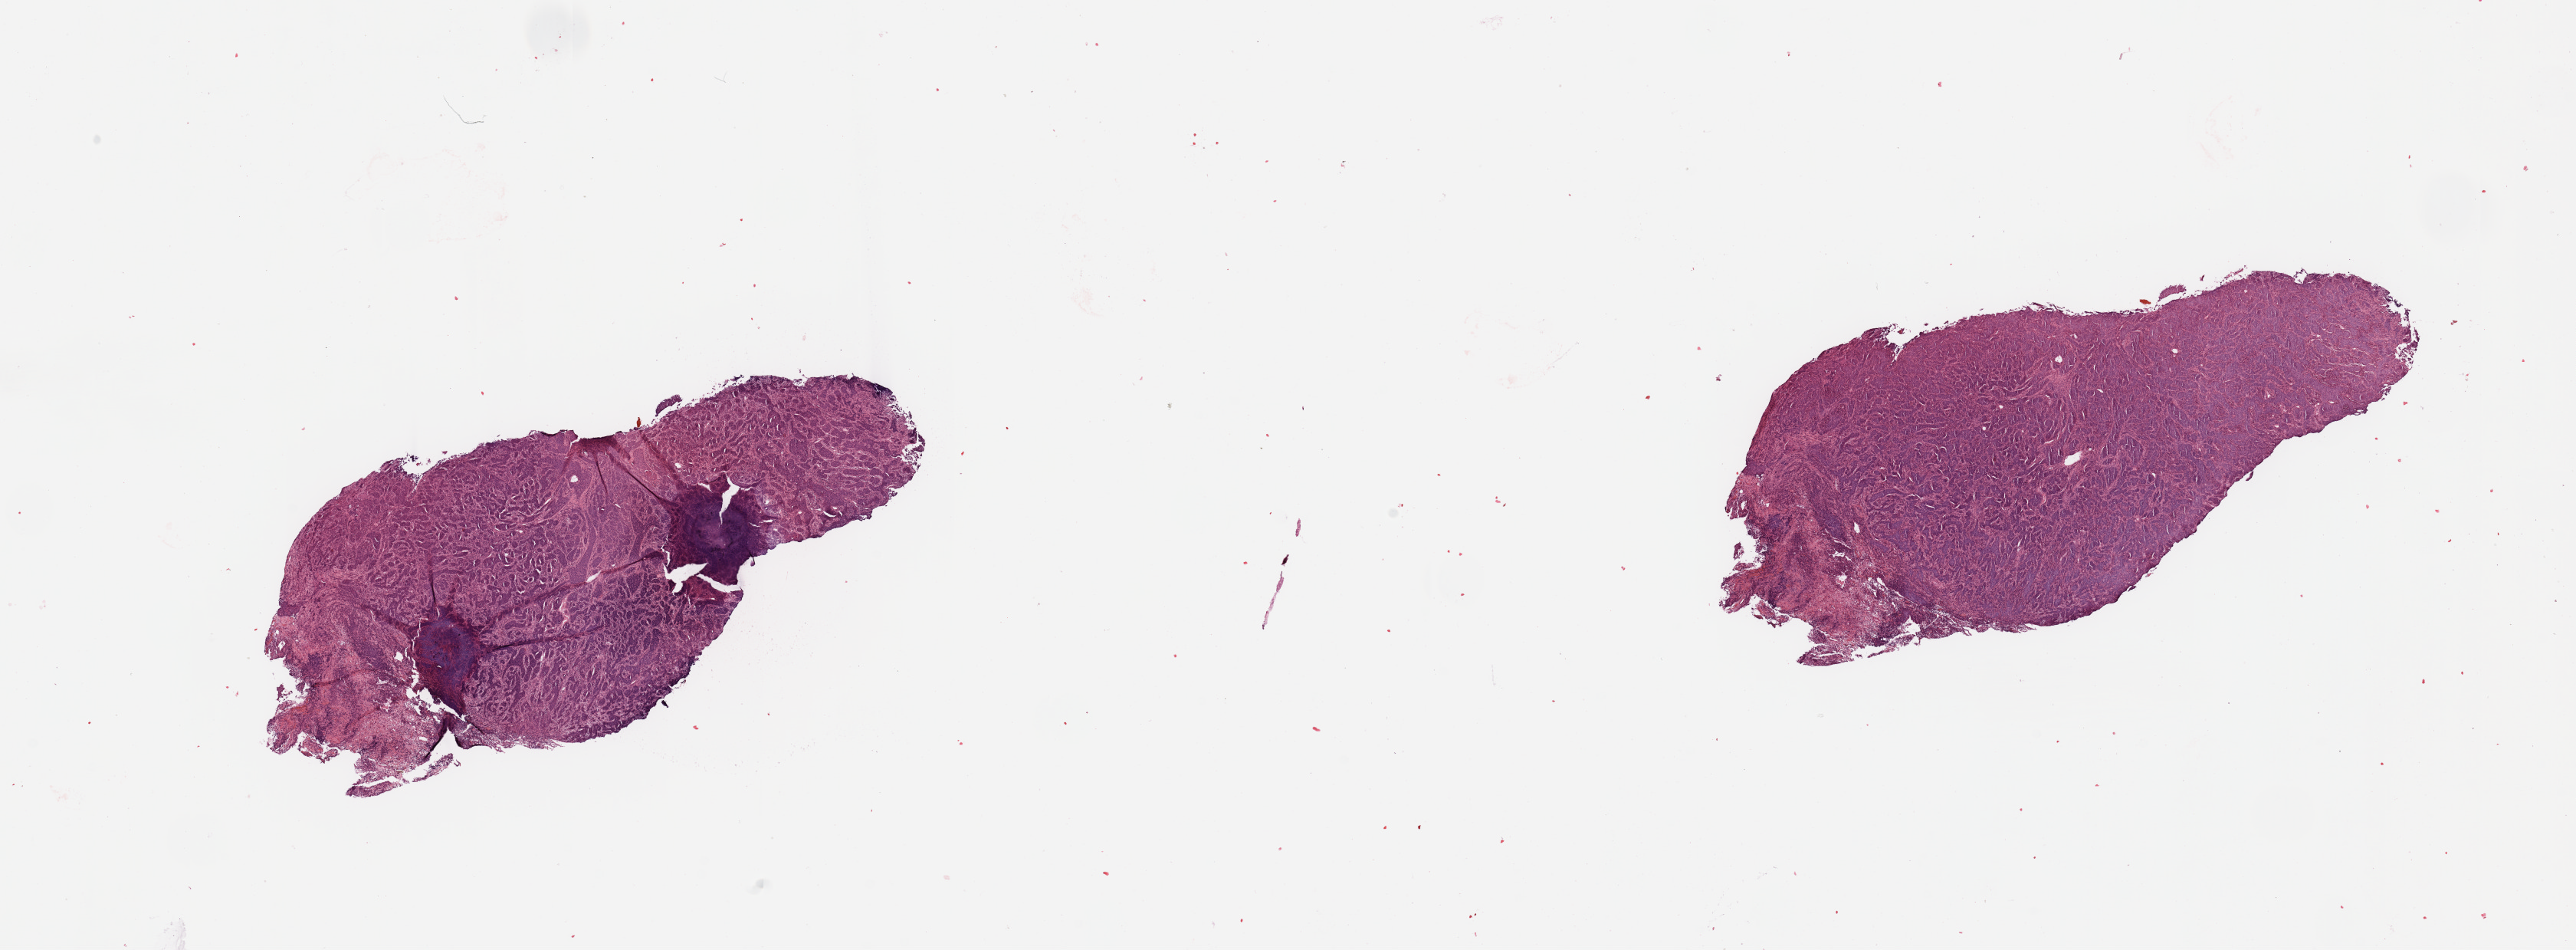
Whole-slide histology image, H&E, shown as a low-resolution overview of the whole scanned area (about 26.6 x 9.8 mm, from a 20x scan), tumour tissue sample, sampled site: lung. 64-year-old female patient. Histologic grade: G2 (moderately differentiated). Composition of this section per pathologist review: tumour nuclei 85%, necrosis 5%.
- histologic diagnosis: Squamous cell carcinoma, NOS
- primary tumour site (as recorded): right middle lobe
- AJCC pathologic stage: IIB